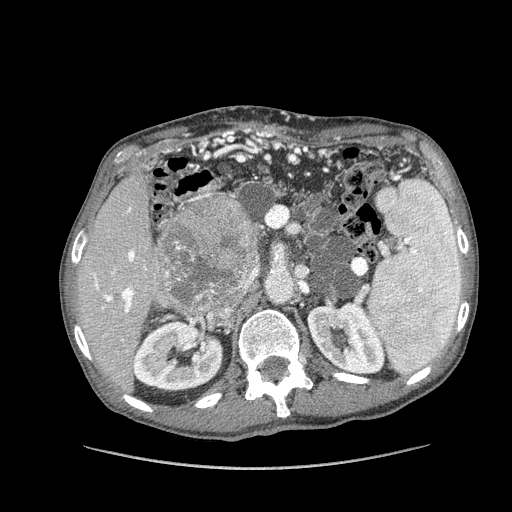
Contrast-enhanced abdominal CT (liver protocol), one axial slice; position 65 of 162 along the scan axis; reconstruction kernel STANDARD; soft-tissue window (W 400 / L 40 HU); 2.5 mm slice thickness; 512 × 512 image matrix, field of view 400 × 400 mm. From the clinical record (not read from this slice): diagnosis: hepatocellular carcinoma (patient treated with transarterial chemoembolisation; whether this scan precedes or follows treatment is not stated here); TNM stage (as recorded): Stage-IIIA; Child-Pugh class: A; tumour nodularity: multinodular.
Structures marked on this image (semi-automatically segmented with operator editing):
- liver parenchyma outside the tumour (the mass and vessels are separate outlines, so this box may not span the whole liver): bounding box <76,167,201,389> (left, top, right, bottom; pixels)
- mass: <157,198,261,313>
- liver vessels: <93,208,146,313>